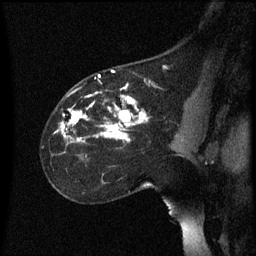
Breast MRI (dynamic contrast-enhanced), one sagittal slice. Position 39 of 60 along the scan axis. Dynamic contrast-enhanced series, image 2 of 3 at this slice position (ordered by acquisition). 1.5 T. TE 4.2 ms, TR 8.4 ms. 2.2 mm slice thickness. 256 × 256 image matrix. Patient: female, 35 years. Case-level facts recorded for this patient, not image findings: setting: breast cancer imaged before/during neoadjuvant chemotherapy; receptor status: HER2-positive.
Annotated regions visible in this slice (semi-automatically segmented with operator editing):
- analysis volume of interest (the breast-tissue region the enhancement analysis was run in; not a lesion): bounding box [x1, y1, x2, y2] px = [42, 72, 178, 173]
- tumour enhancement mask (voxels above the 70 % enhancement threshold inside the analysis volume of interest): [57, 76, 147, 143]